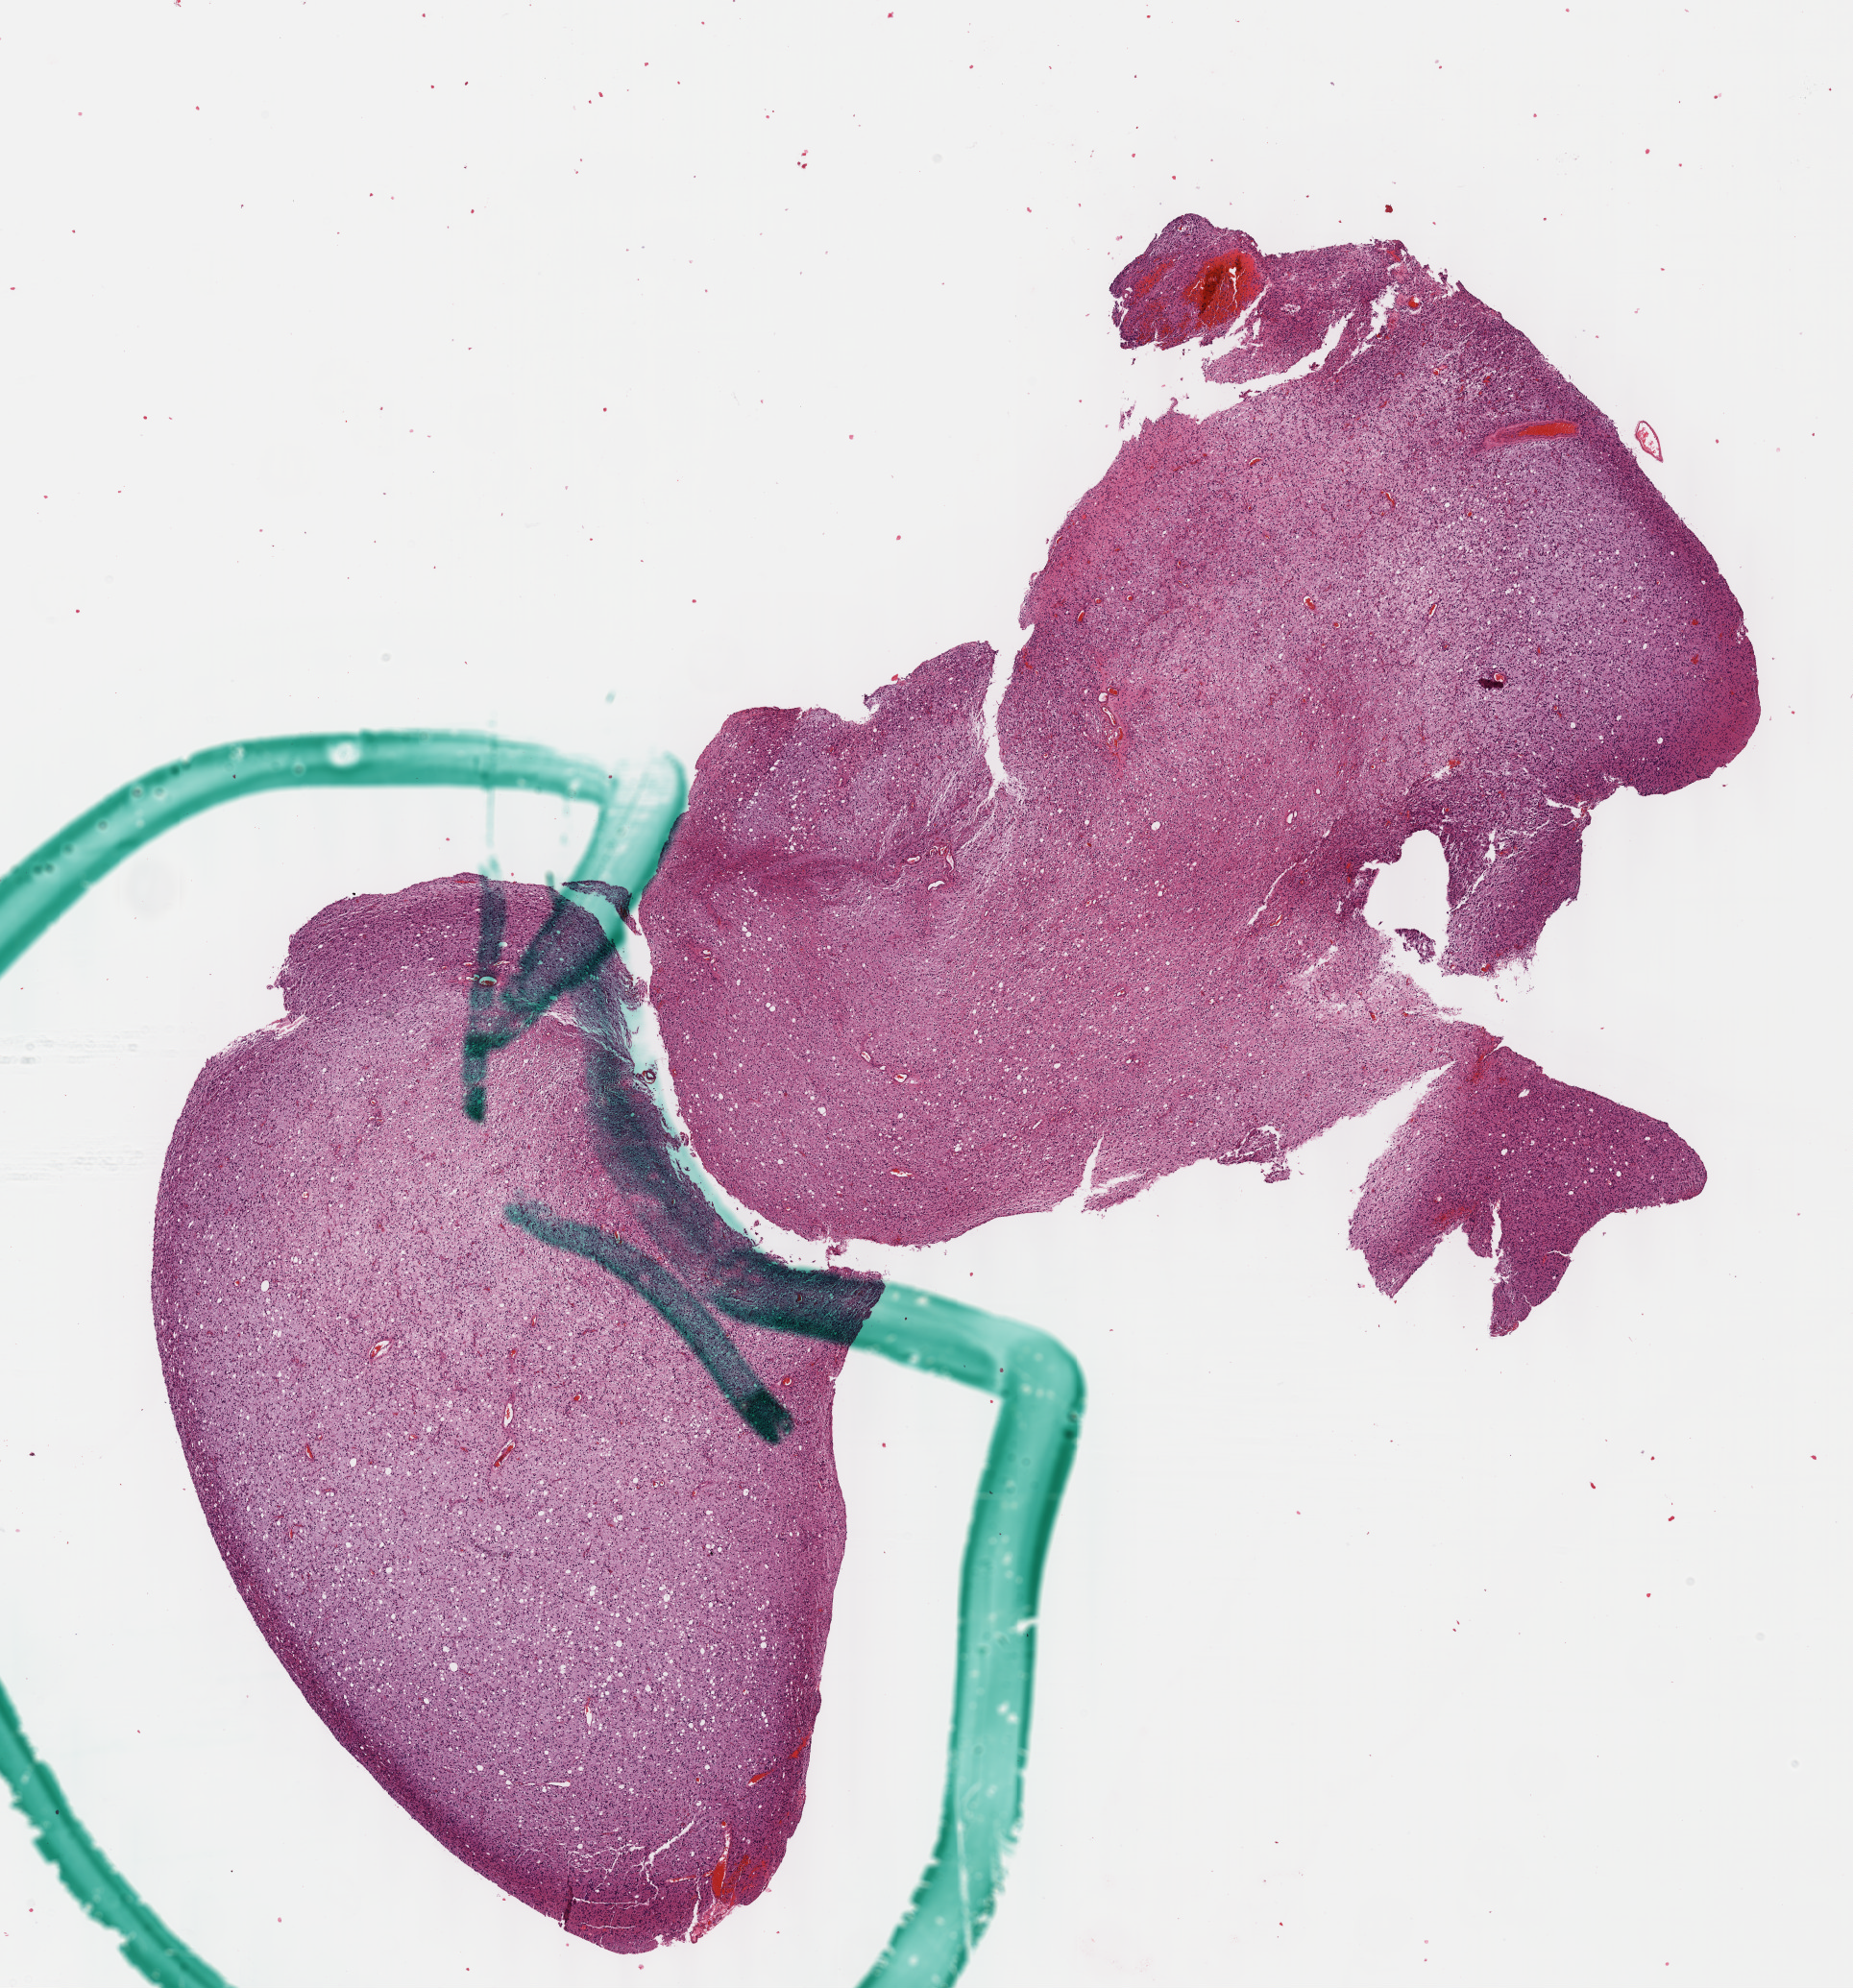
H&E whole-slide image, shown as a low-resolution overview of the whole scanned area (about 15.6 x 16.7 mm, from a 40x scan). Formalin-fixed paraffin-embedded (FFPE) diagnostic section. Brain, primary tumour sample. Male patient; age at initial diagnosis 24 years. Histologic grade: G2 (moderately differentiated).
• pathologic diagnosis: Astrocytoma, NOS